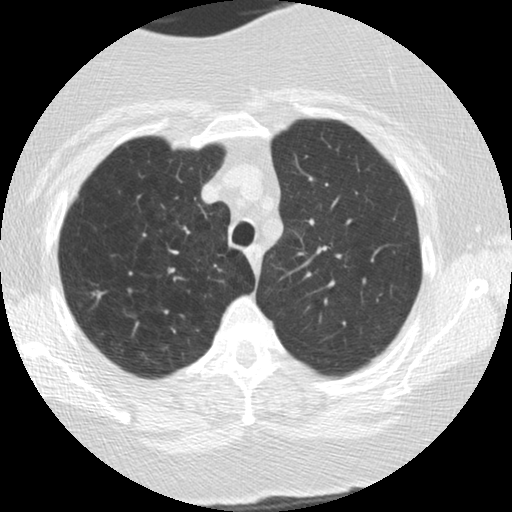
Low-dose screening chest CT, one axial slice; slice 136 of 166 in the series (ordered by position); lung window (W 1500 / L -600 HU); 2.5 mm slice thickness; 512 × 512 image matrix, field of view 309 × 309 mm.
Outlined on this slice (expert manual segmentation):
- lesion 2 (tumor, upper lobe of right lung): box from (x=97, y=291) to (x=104, y=299) px